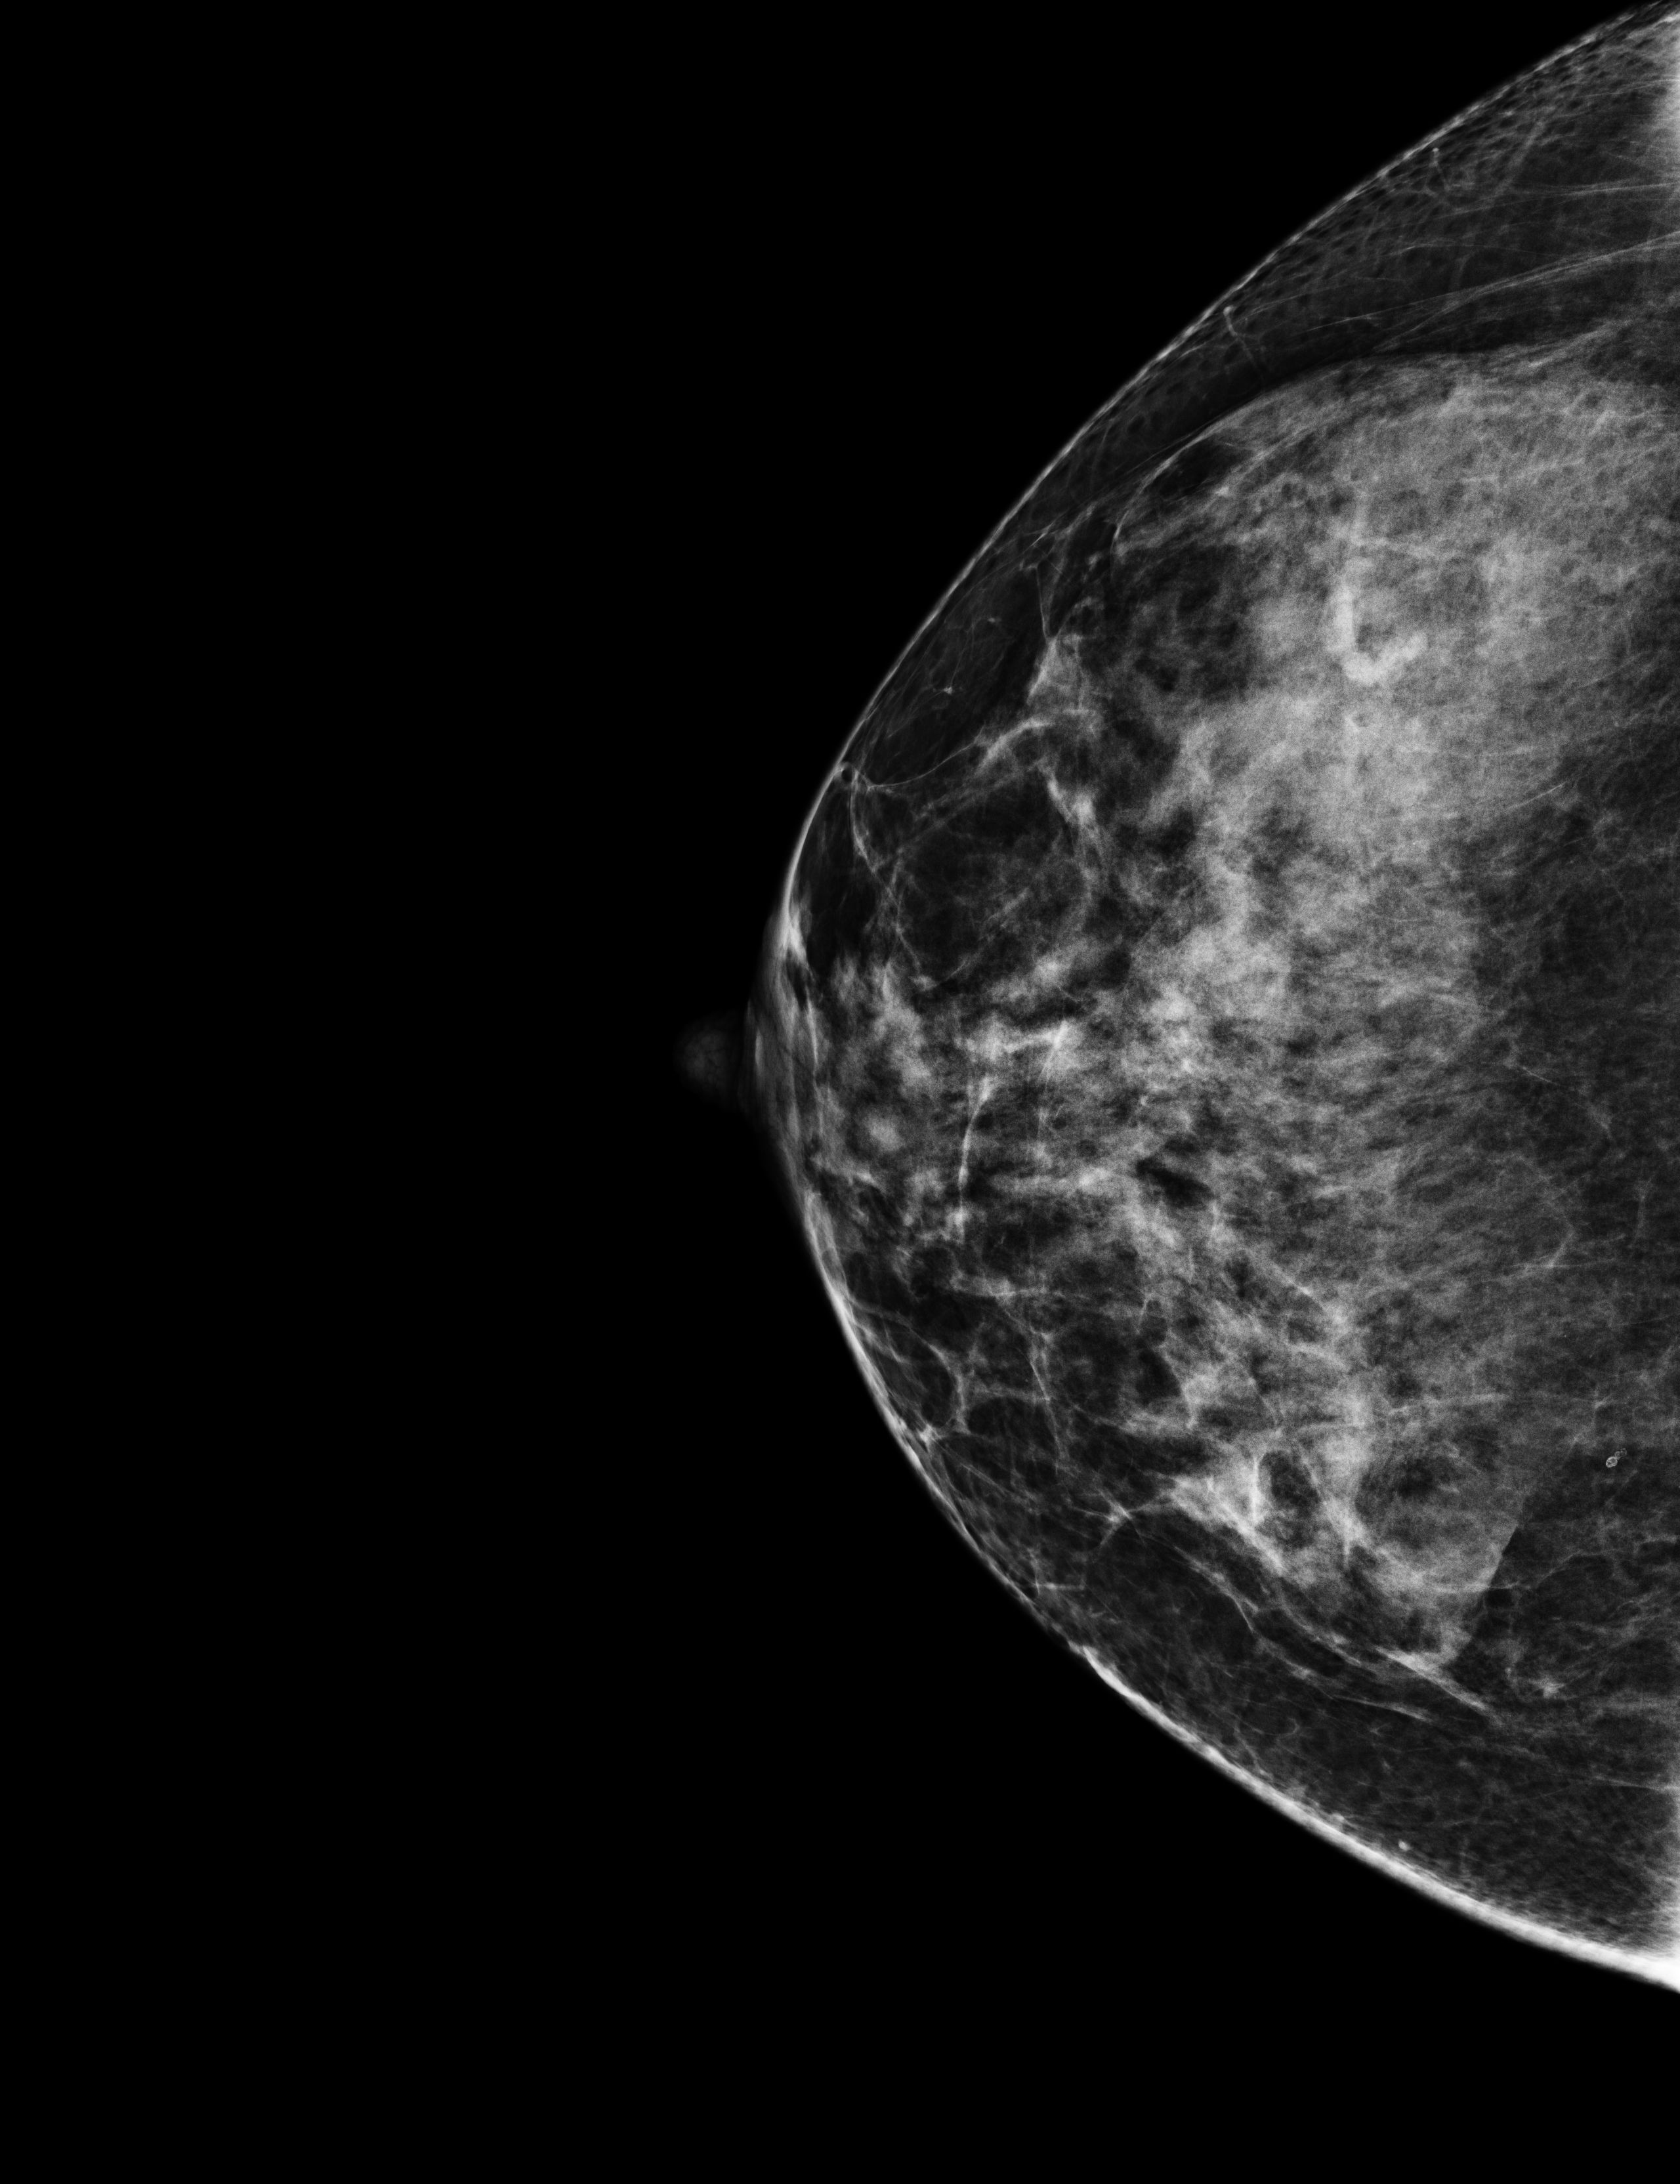
Screening examination, compressed breast thickness 69 mm. Female patient, age 47 years.
Image type: full-field digital mammogram. Breast: right. Projection: craniocaudal (CC) view.